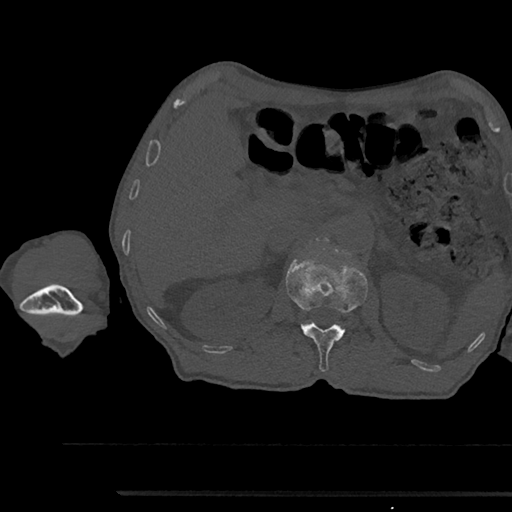
CT including the spine, one axial slice; position 628 of 797 along the scan axis; reconstruction kernel Br40s/3; 120 kVp; bone window (W 1800 / L 400 HU); 512 × 512 image matrix, field of view 367 × 367 mm. Male patient, age 79 years. Case-level facts recorded for this patient, not image findings: primary cancer: prostate.
Structures marked on this image (semi-automatically segmented with operator editing):
- L1 vertebra: bounding box <285,254,368,372> (left, top, right, bottom; pixels)
- L2 vertebra: <316,238,328,241>